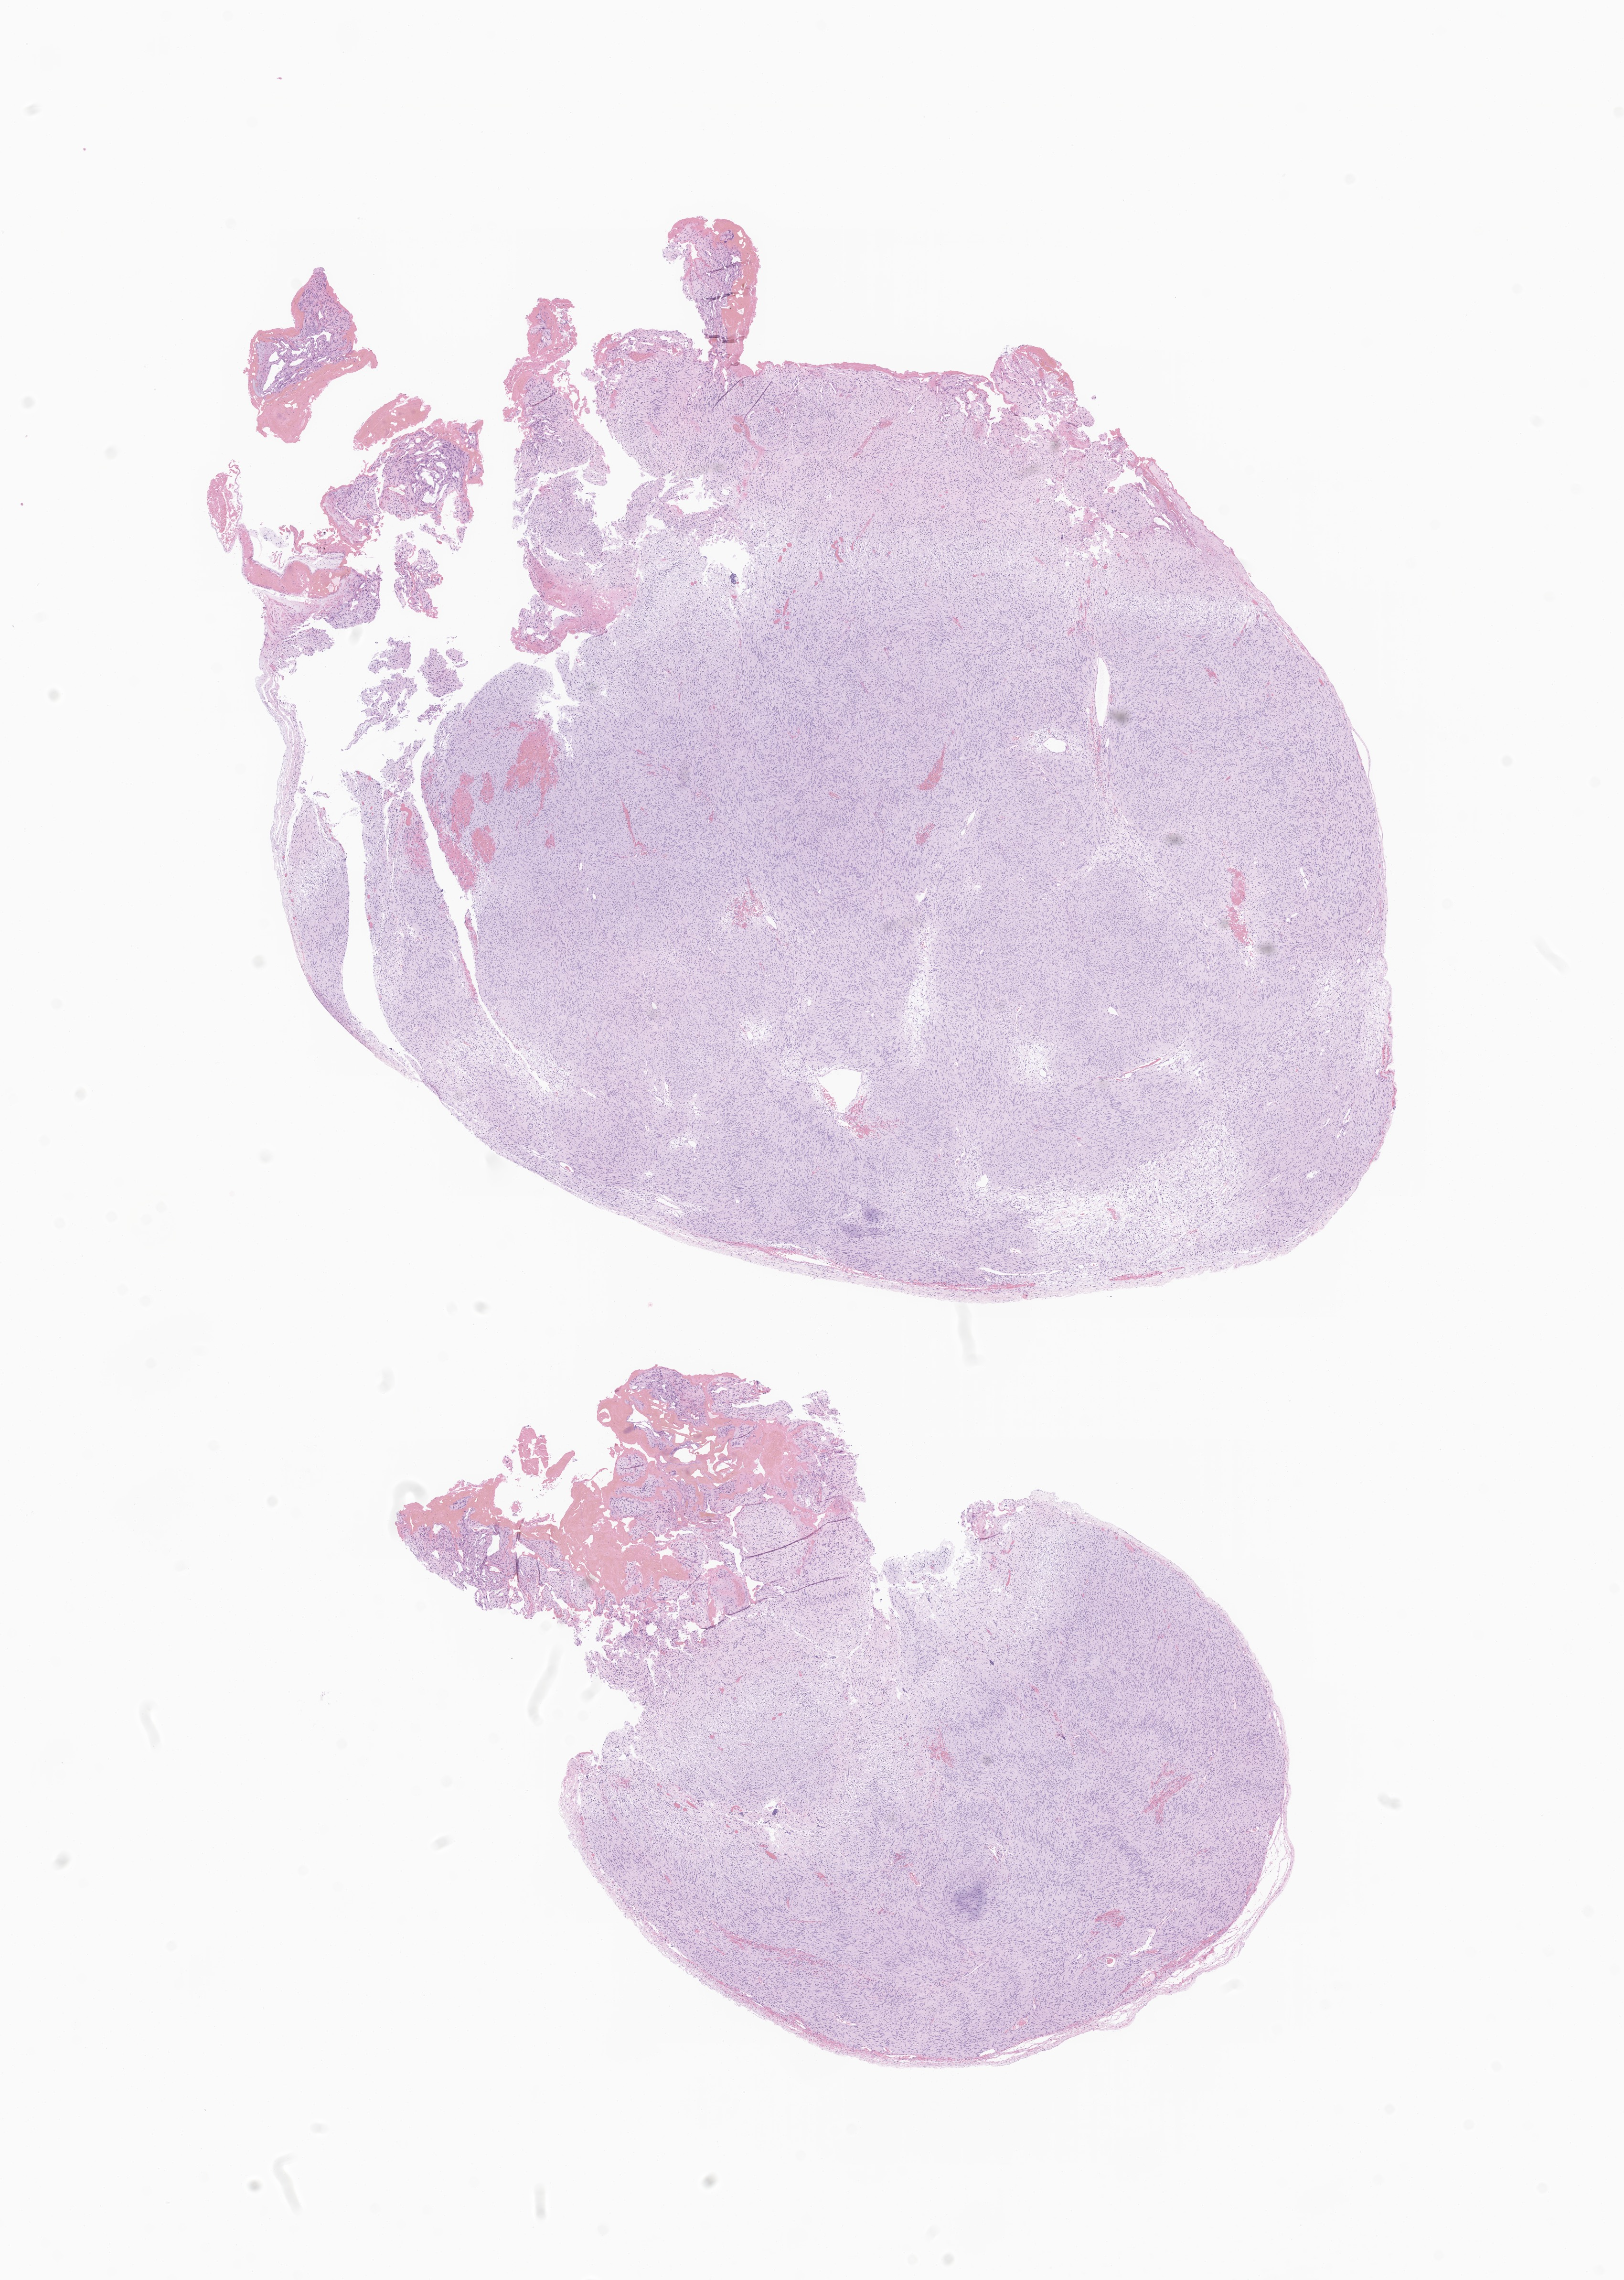
Digitized haematoxylin and eosin-stained section of tumor tissue from the brain — shown as a low-resolution overview of the whole scanned area (about 14.3 x 20.1 mm), formalin-fixed, paraffin-embedded (FFPE) tissue. Patient: male, age 176 months (14 years 8 months).
• diagnosis: Schwannoma, NOS